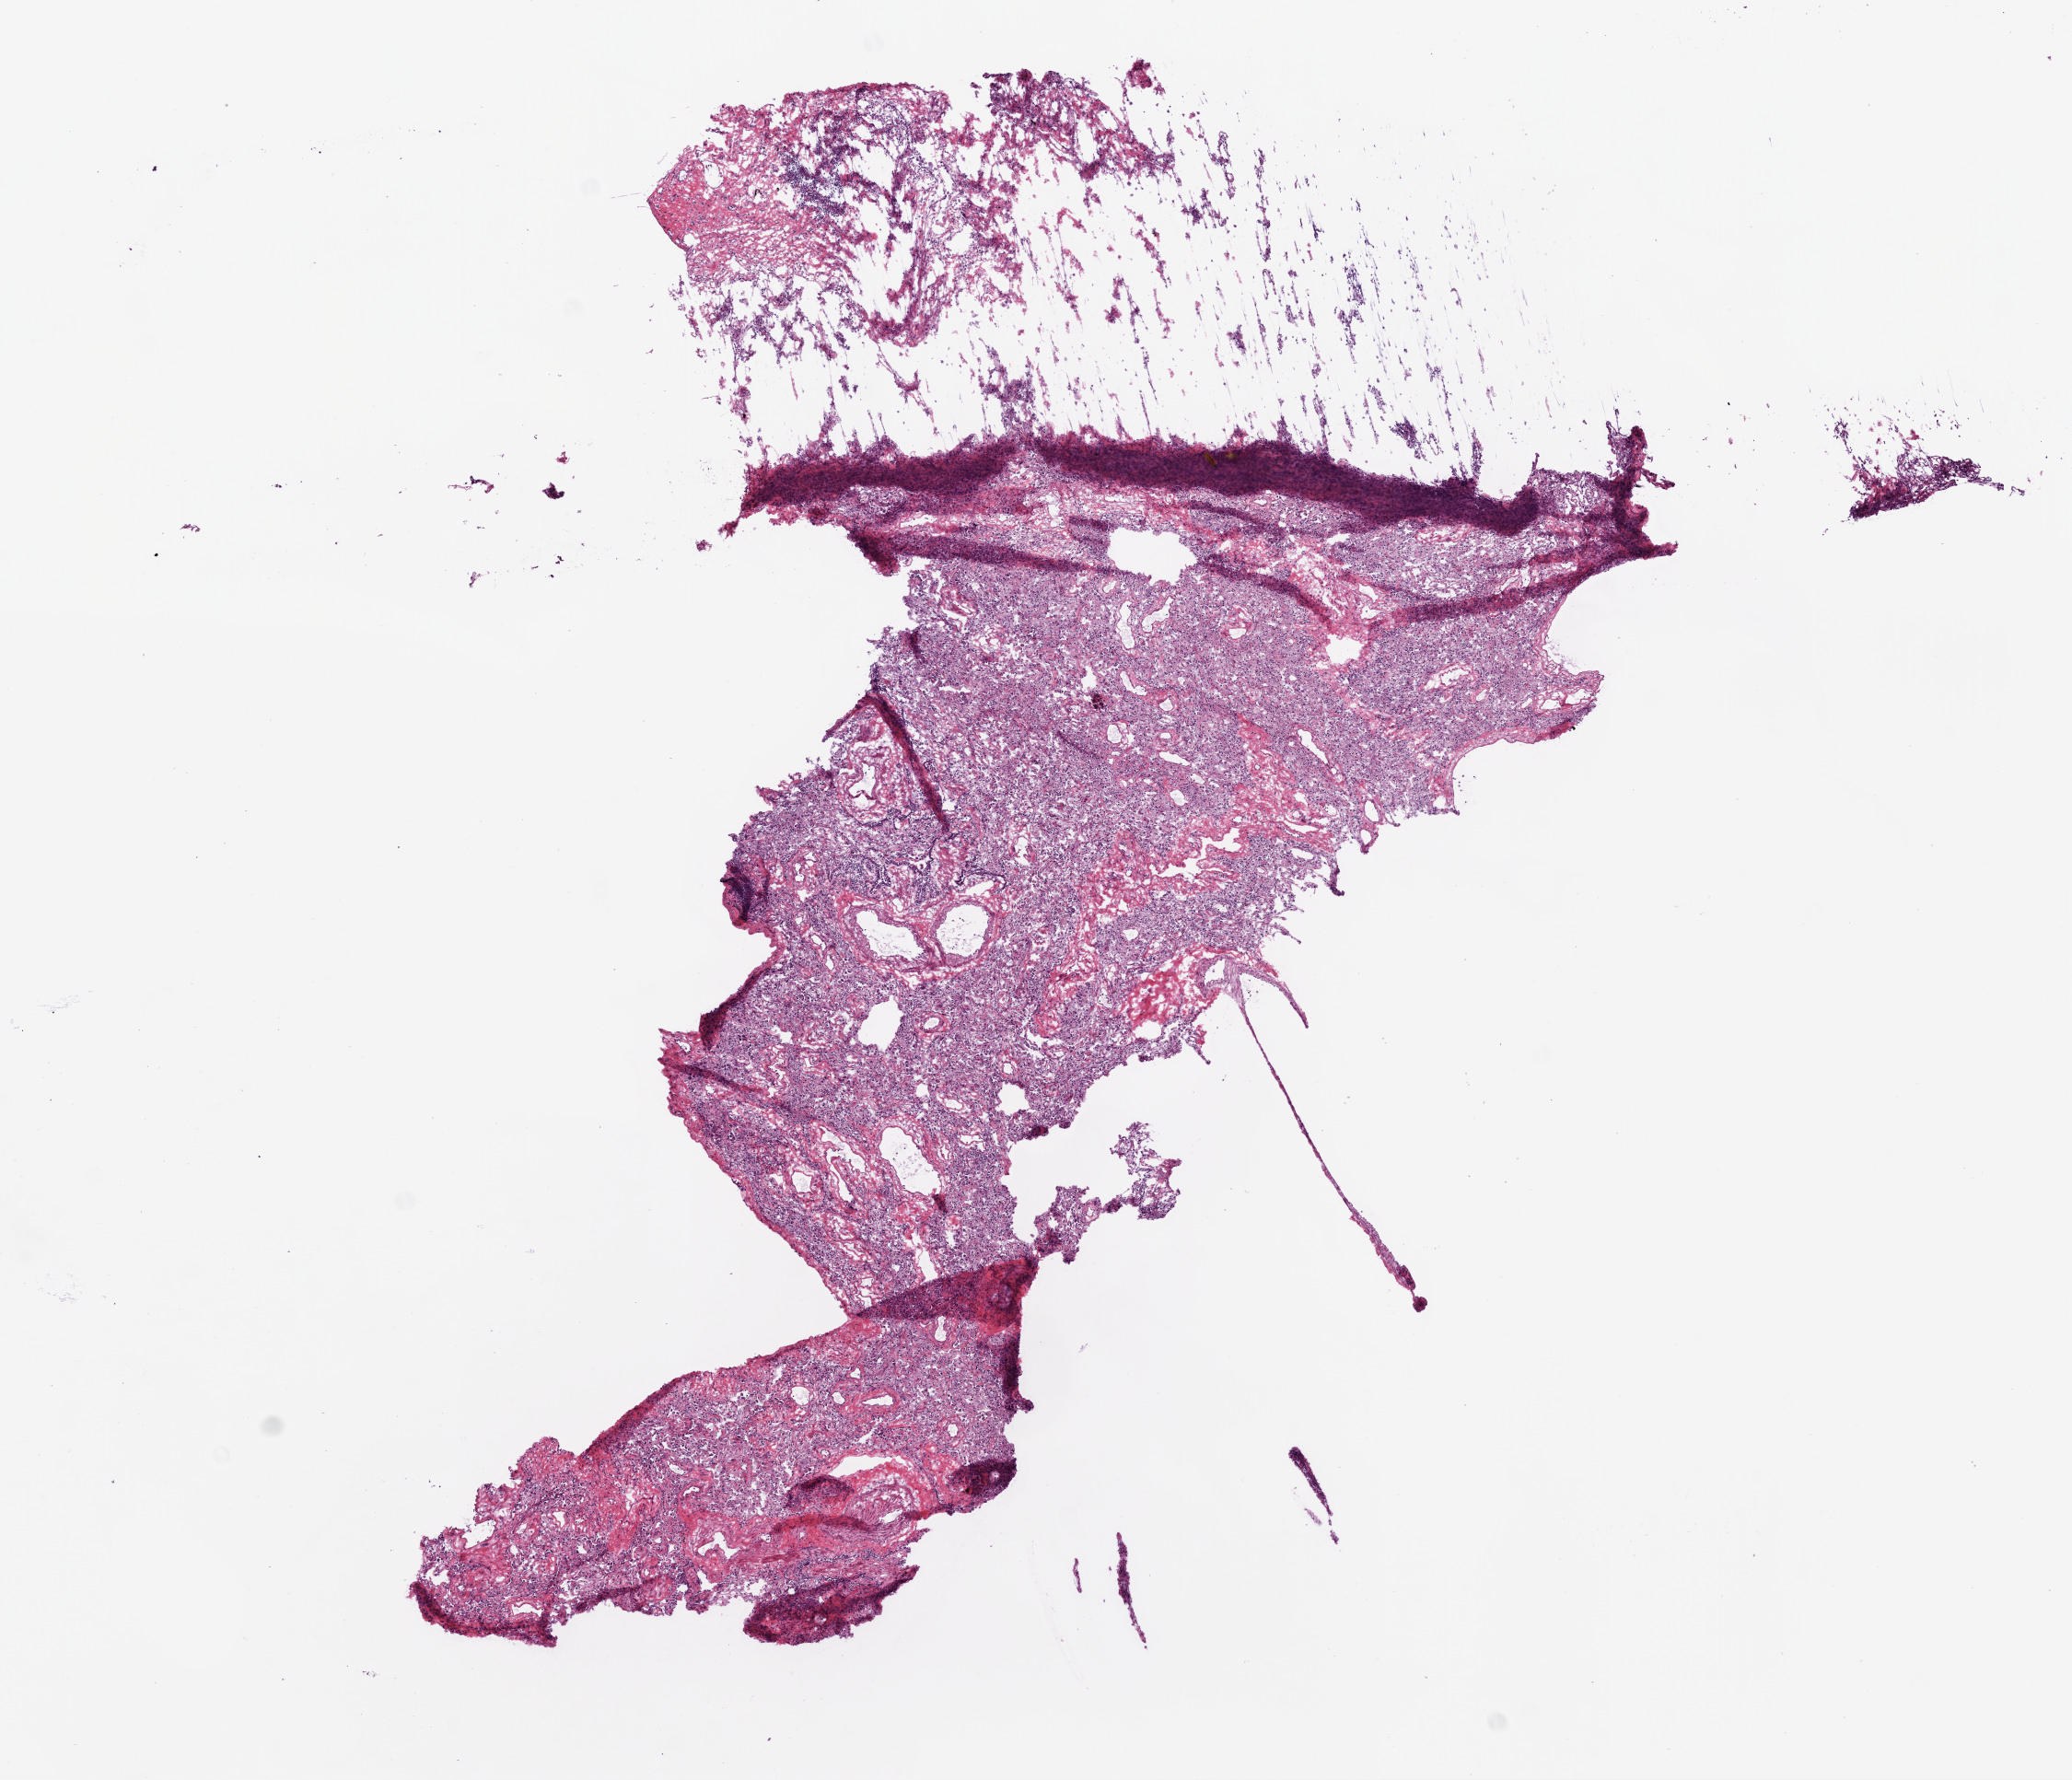
Whole-slide histology image, Hematoxylin and eosin (H&E) stained — whole scanned area (about 9.0 x 7.8 mm, from a 20x scan) shown as a low-resolution overview. Frozen section from the bottom of the tissue portion. Sample: solid tissue normal (non-tumour tissue), lung. Male patient; age at initial diagnosis 71 years.
• this section: solid tissue normal sample (biorepository sample class)
• patient diagnosis: Squamous cell carcinoma, NOS (lower lobe, lung)